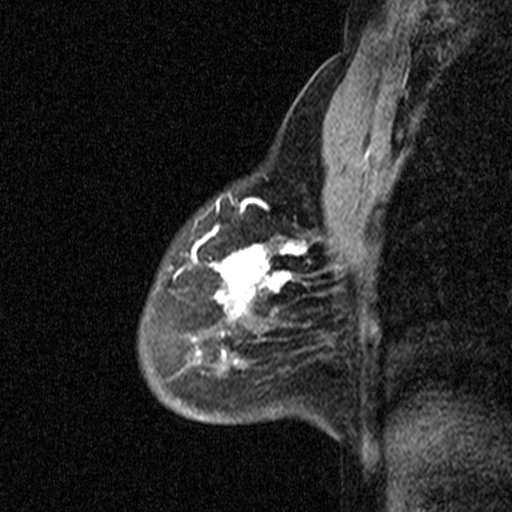
Breast MRI (dynamic contrast-enhanced), one sagittal slice. Slice 32 of 44 in the series (ordered by position). Dynamic contrast-enhanced study with each time point stored as its own series, time point 2 of 3 at this slice position (early post-contrast, ordered by acquisition time). 1.5 T. TE 4.5 ms, TR 11 ms. 512 × 512 image matrix, field of view 200 × 200 mm. Patient: female, 53 years. Case-level facts recorded for this patient, not image findings: setting: breast cancer imaged before/during neoadjuvant chemotherapy; receptor status: HR-positive, HER2-negative.
Annotated regions visible in this slice (semi-automatic segmentation, software-assisted and operator-edited):
- analysis volume of interest (the breast-tissue region the enhancement analysis was run in; not a lesion): bounding box [x1, y1, x2, y2] px = [88, 176, 313, 423]
- tumour enhancement mask (voxels above the 90 % enhancement threshold inside the analysis volume of interest): [175, 197, 306, 354]